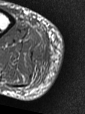
MRI of an extremity soft-tissue mass, one axial slice; slice 8 of 47 in the series (ordered by position); MR volume resampled by the dataset authors to the PET/CT grid (not the native acquisition matrix); 3.27 mm slice thickness; 85 × 114 image matrix, field of view 83 × 111 mm. Male patient. Case-level facts recorded for this patient, not image findings: histological type: pleiomorphic liposarcoma; grade: high; site of the primary tumour: right calf.
Structures marked on this image (expert contour drawn on MRI and transferred to this co-registered scan by the dataset authors):
- gross tumour volume including surrounding oedema: bounding box [x1, y1, x2, y2] px = [33, 53, 41, 61]